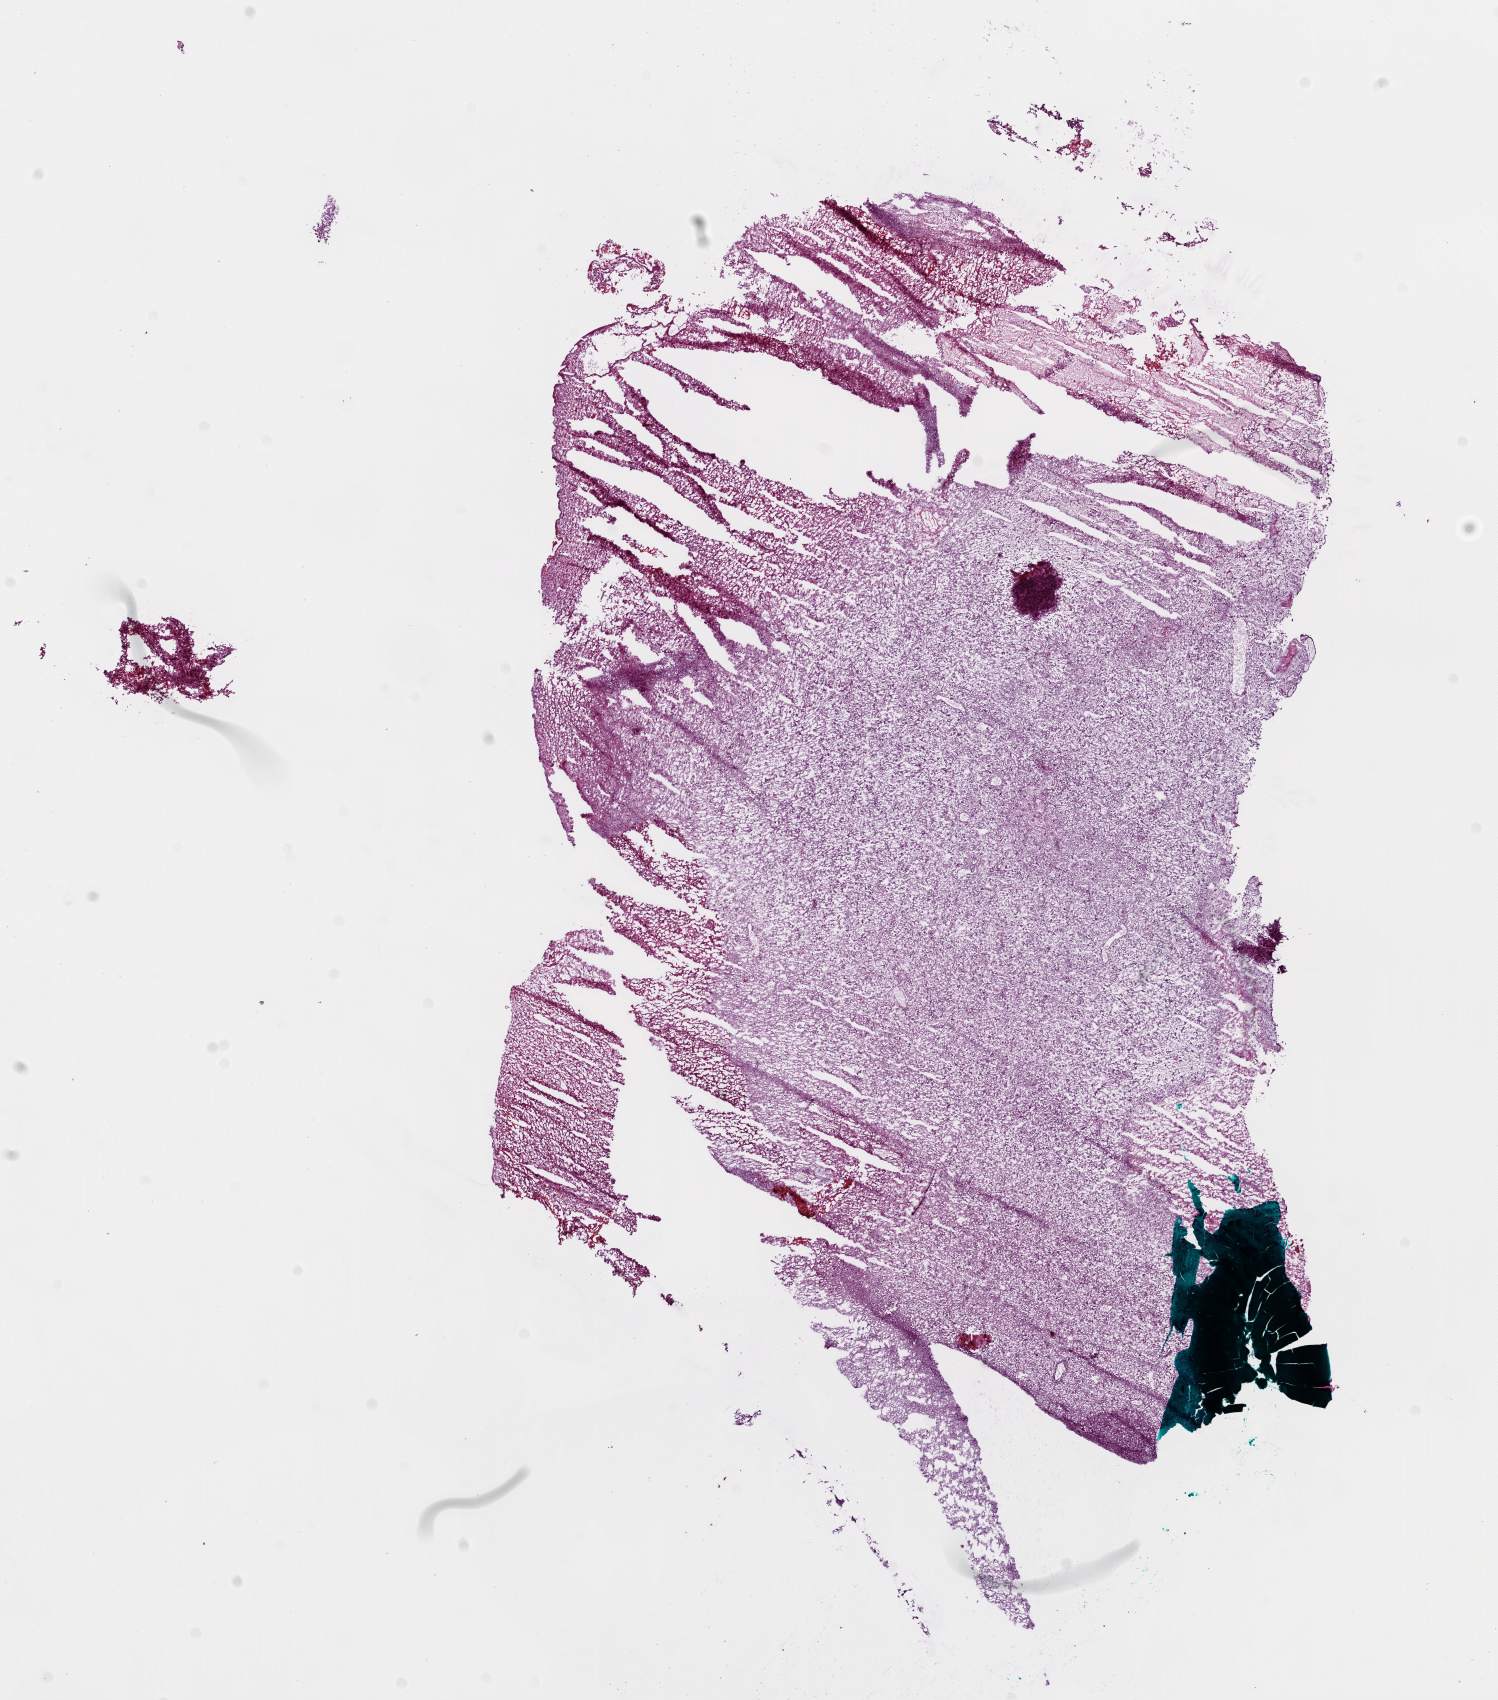
Digitized H&E tissue section (whole slide) — a low-resolution overview of the entire scanned area, about 12.1 x 13.7 mm (slide scanned at 20x). Frozen section from the bottom of the tissue portion. Sample: primary tumour, brain. Female patient; age at initial diagnosis 66 years. Composition of this section per pathologist review: tumour cells 80%, tumour nuclei 85%, stromal cells 10%, necrosis 10%.
Pathologic diagnosis: Glioblastoma.